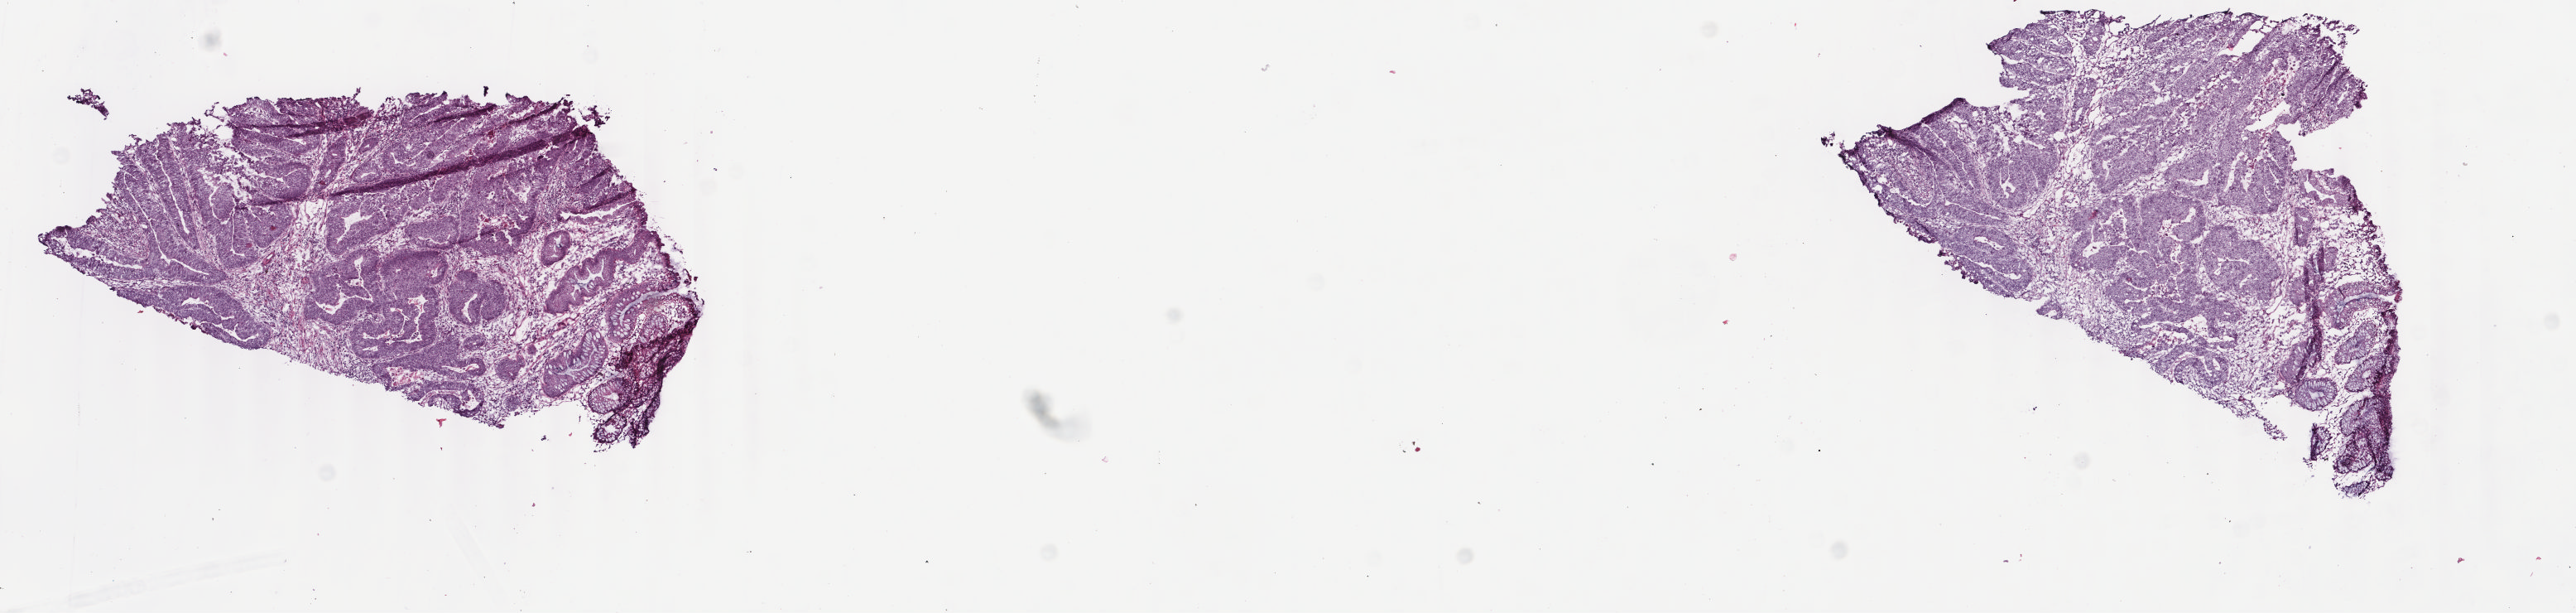
Hematoxylin and eosin (H&E) stained whole-slide image, a low-resolution overview of the entire scanned area, about 12.4 x 2.9 mm (from a 40x scan); frozen section from the bottom of the tissue portion; primary tumour sample from the colon. Male, age 70 years at initial diagnosis. Pathologist review of this section (percent, as recorded): tumour cells 92%, tumour nuclei 90%, normal cells 0%, stromal cells 7%, necrosis 1%. Inflammatory infiltration, as recorded: lymphocyte infiltration 2%, monocyte infiltration 1%, neutrophil infiltration 1%.
TNM: T3 N0 M0. AJCC pathologic stage: IIA (6th edition). Pathologic diagnosis: Adenocarcinoma, NOS (sigmoid colon).